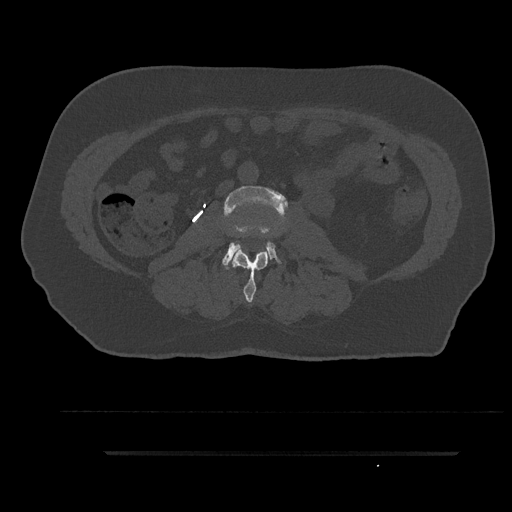
CT including the spine, one axial slice; slice 74 of 797 in the series (ordered by position); reconstruction kernel Br40s/3; bone window (W 1800 / L 400 HU); 512 × 512 image matrix. Male patient, age 63 years. From the clinical record (not read from this slice): primary cancer: renal; vertebrae with lytic lesions (as recorded): T8.
Structures marked on this image (semi-automatic segmentation, software-assisted and operator-edited):
- L2 vertebra: bounding box (x1, y1, x2, y2) in pixels: (232, 250, 268, 302)
- L3 vertebra: (222, 185, 288, 268)